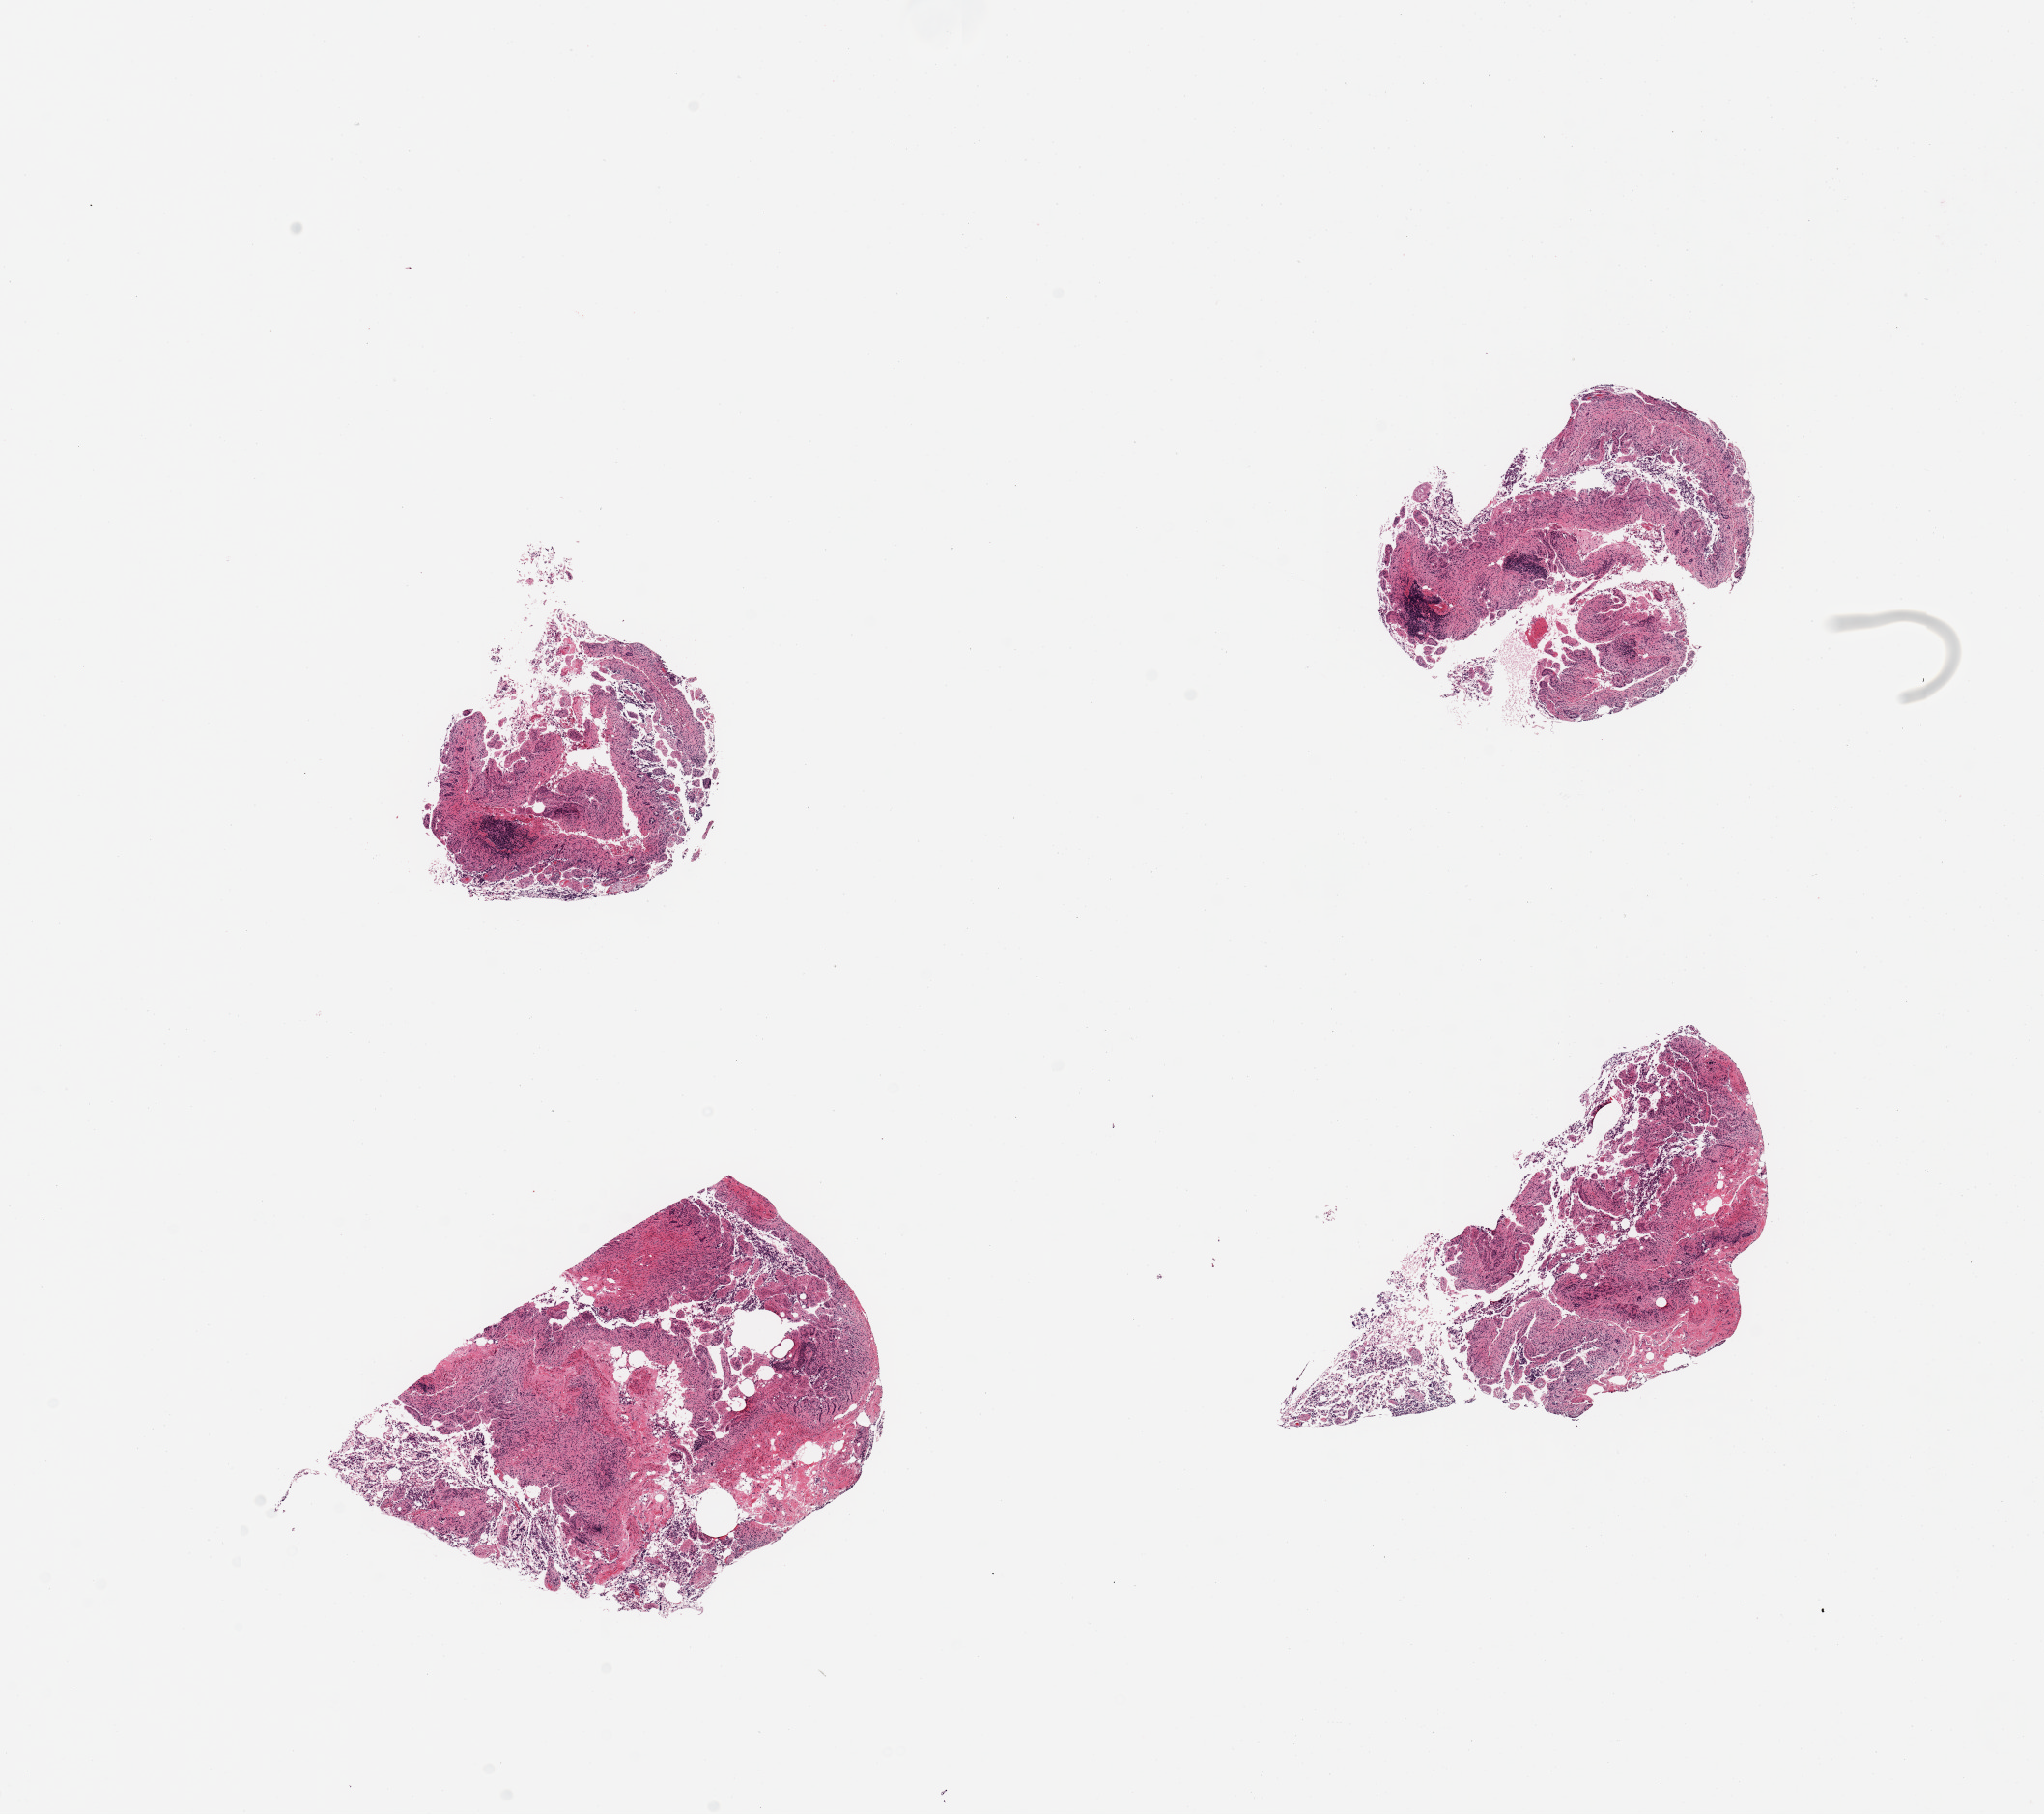
Whole-slide image, H&E stain, brightfield — shown as a low-resolution overview of the whole scanned area (about 16.7 x 14.9 mm).
Specimen: PAXgene-fixed paraffin-embedded (PFPE) section; target tissue: ileum; tissue donor sample.